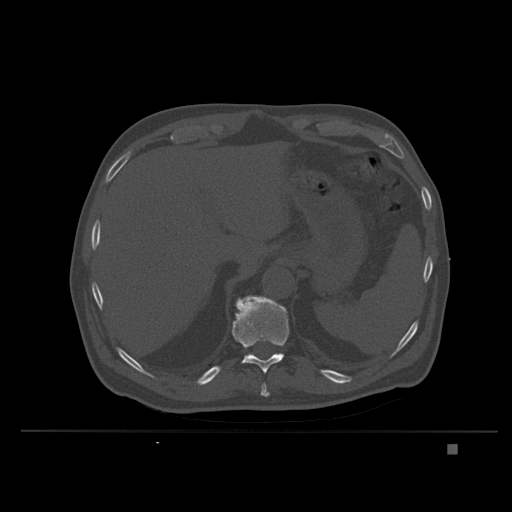
CT including the spine, one axial slice; position 176 of 435 along the scan axis; bone window (W 1800 / L 400 HU); 1.5 mm slice thickness; 512 × 512 image matrix. Patient: male, 73 years. Case-level facts recorded for this patient, not image findings: primary cancer: skin.
Outlined on this slice (semi-automatic segmentation, software-assisted and operator-edited):
- T10 vertebra: bounding box (x1, y1, x2, y2) in pixels: (261, 383, 270, 397)
- T11 vertebra: (232, 296, 289, 373)